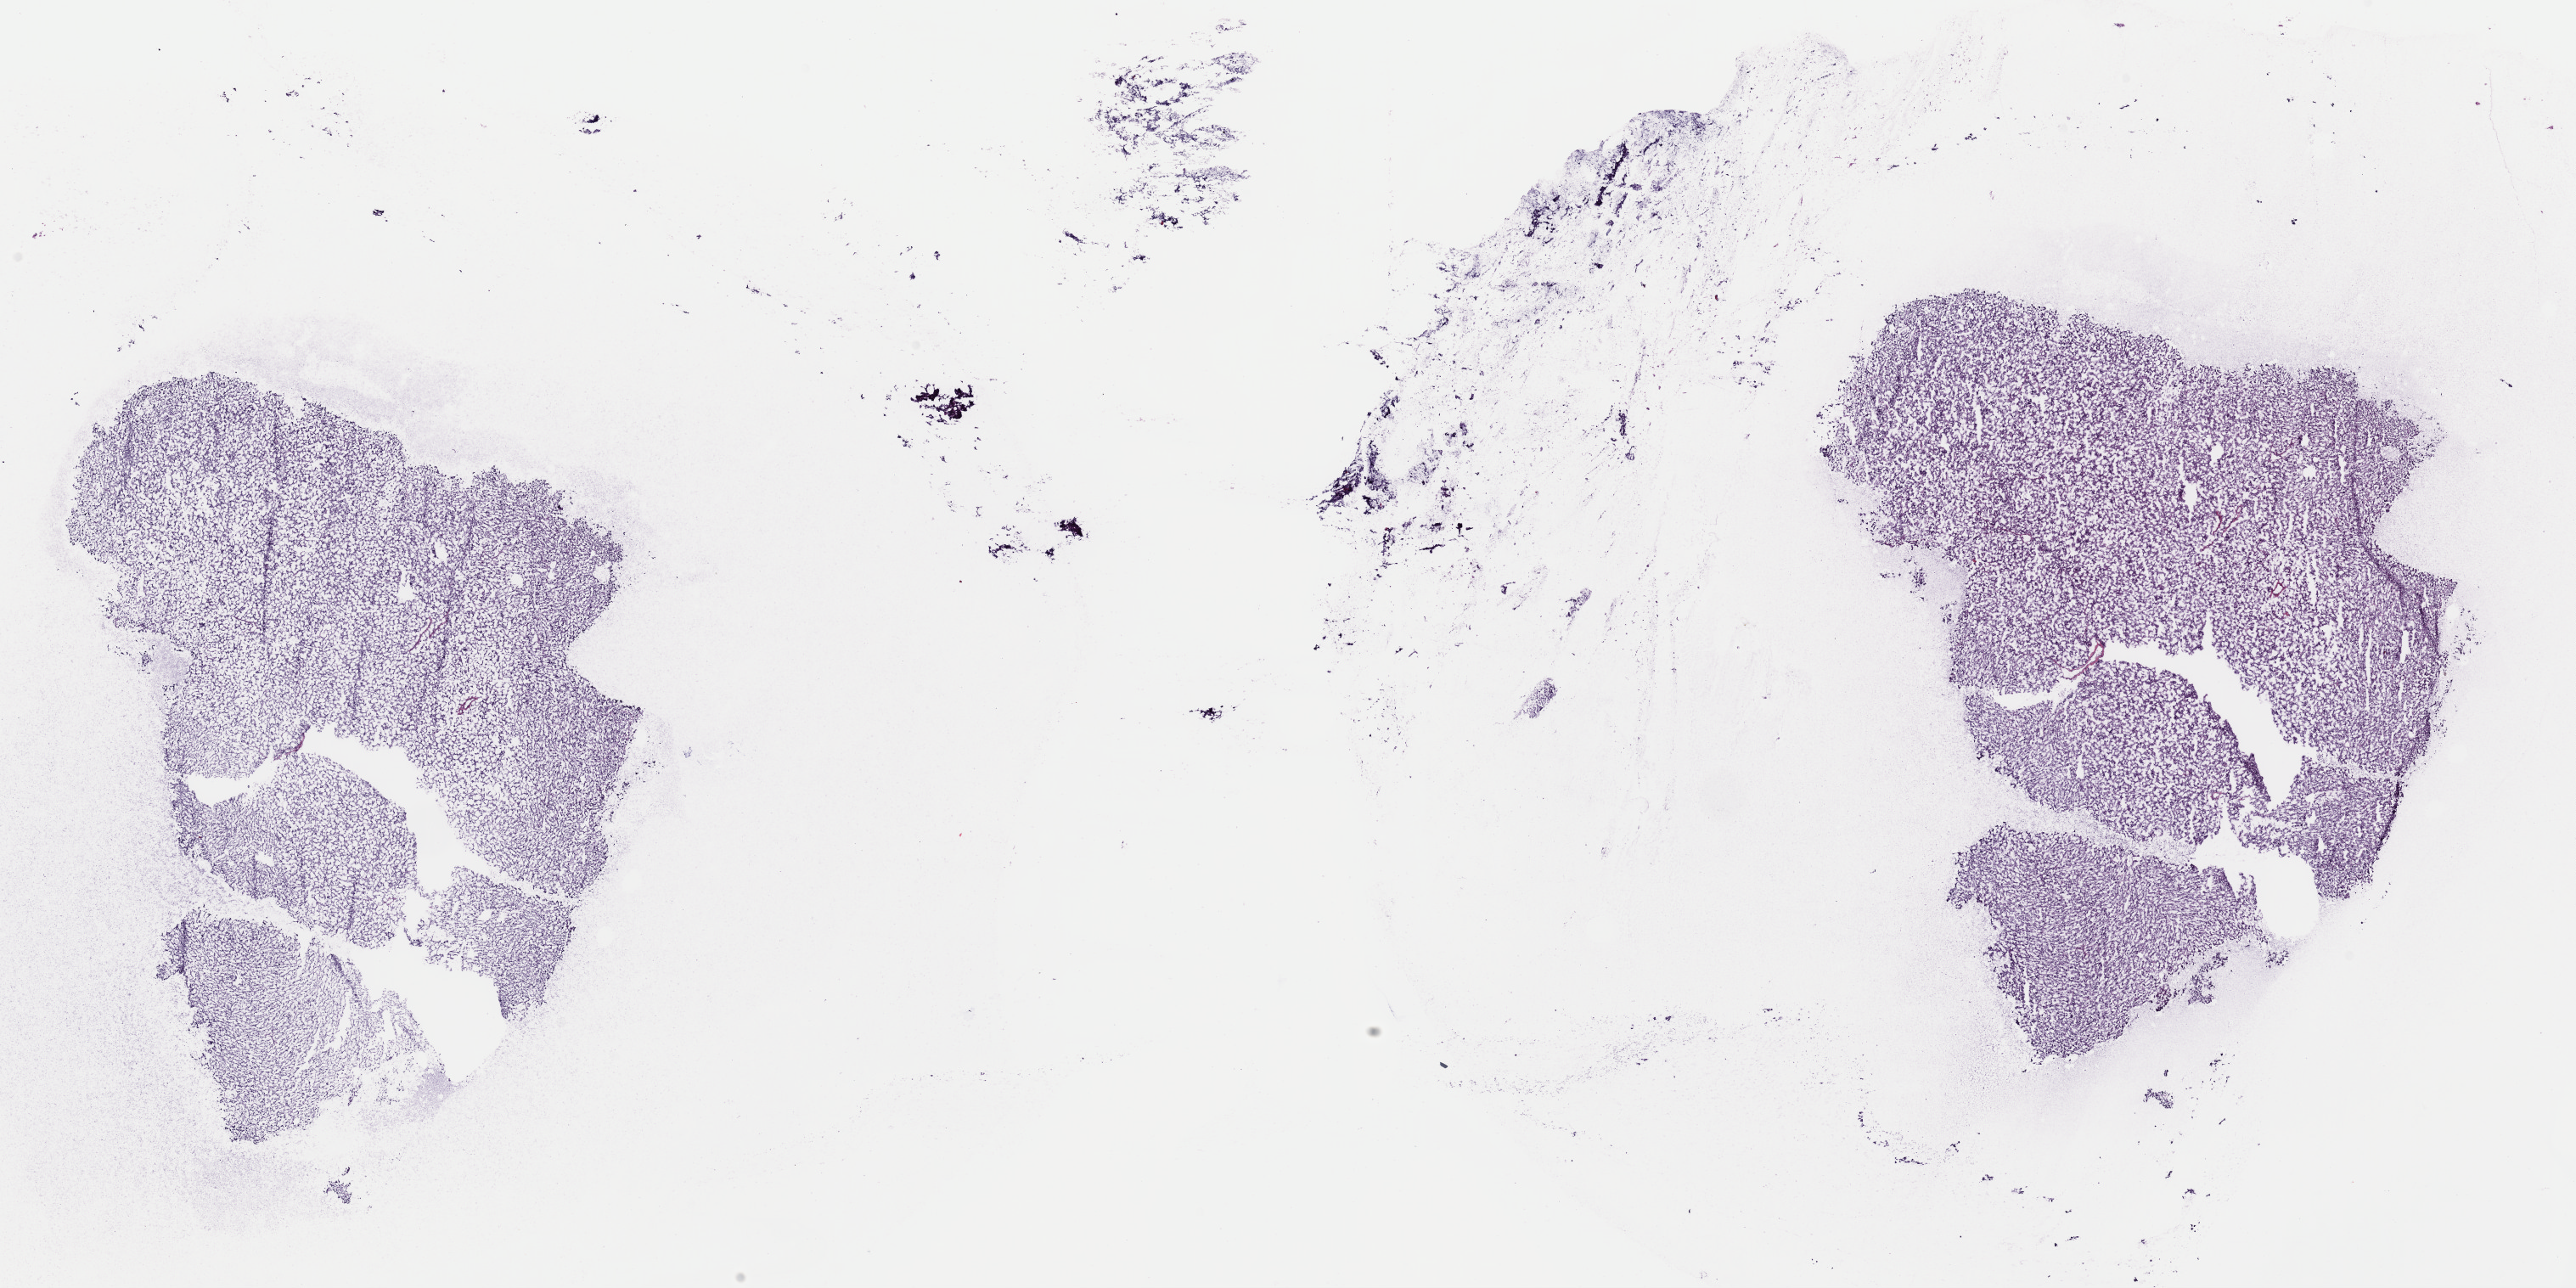
H&E-stained whole-slide image, shown as a low-resolution overview of the whole scanned area (about 24.0 x 12.0 mm, from a 40x scan); frozen section from the top of the tissue portion; adrenal gland, primary tumour sample. Male patient; age at initial diagnosis 38 years. Pathologist review of this section (percent, as recorded): tumour cells 95%, tumour nuclei 100%, normal cells 0%, stromal cells 5%, necrosis 0%. Infiltration values recorded for this section: lymphocyte infiltration 0%, monocyte infiltration 0%, neutrophil infiltration 0%.
Diagnosis: Pheochromocytoma, NOS.